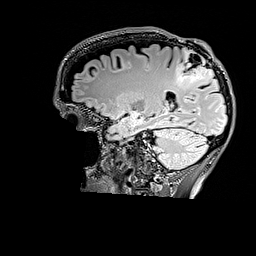
Brain MRI from a brain-tumour surgery series, one sagittal slice; slice 112 of 176 in the series (ordered by position); T2 FLAIR; 256 × 256 image matrix, field of view 256 × 256 mm. From the clinical record (not read from this slice): histopathology: Astrocytoma; WHO grade: 3; IDH mutation: yes.
Outlined on this slice (manually delineated by an expert):
- tumour: bounding box [x1, y1, x2, y2] px = [175, 50, 215, 86]
- tumour: [187, 59, 214, 82]